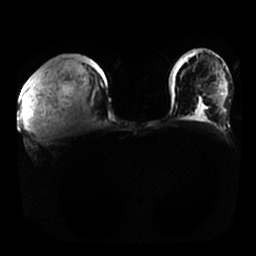
Breast MRI, one axial slice. Position 9 of 25 along the scan axis. Diffusion-weighted series; image 2 of 4 stored at this slice position (different b-values; order by instance number). 1.5 T. 4 mm slice thickness. 256 × 256 image matrix, field of view 350 × 350 mm. Female patient.
Annotated regions visible in this slice (manually delineated by an expert):
- tumour on diffusion-weighted imaging: box from (x=25, y=83) to (x=36, y=131) px